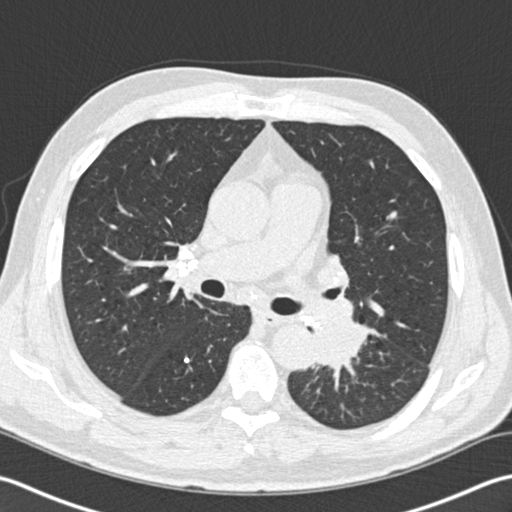
Low-dose screening chest CT, one axial slice; slice 103 of 170 in the series (ordered by position); reconstruction kernel B30f; 120 kVp; lung window (W 1500 / L -600 HU); 512 × 512 image matrix.
Annotated regions visible in this slice (outlined manually by an expert reader):
- lesion 1 (tumor, lower lobe of left lung): bounding box <317,319,367,370> (left, top, right, bottom; pixels)